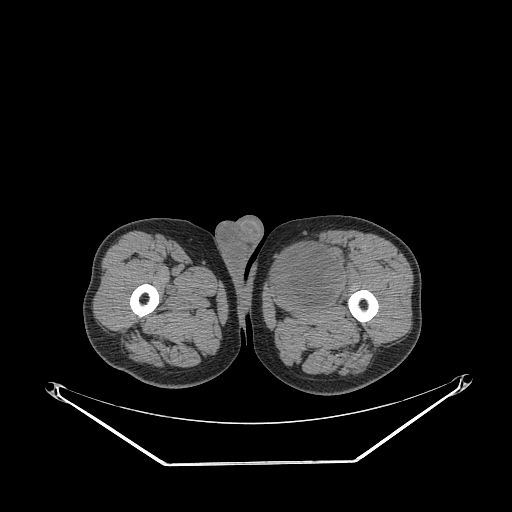
CT of an extremity soft-tissue mass (from a PET/CT study), one axial slice. Position 258 of 267 along the scan axis. Reconstruction kernel STANDARD. 140 kVp. Soft-tissue window (W 400 / L 40 HU). 3.75 mm slice thickness. 512 × 512 image matrix, field of view 500 × 500 mm. Male patient. Case-level facts recorded for this patient, not image findings: histological type: pleiomorphic liposarcoma; grade: high; site of the primary tumour: left thigh.
Outlined on this slice (expert contour drawn on MRI and transferred to this co-registered scan by the dataset authors):
- gross tumour volume including surrounding oedema: bounding box (x1, y1, x2, y2) in pixels: (276, 237, 348, 300)
- gross tumour volume (mass): (276, 246, 341, 300)